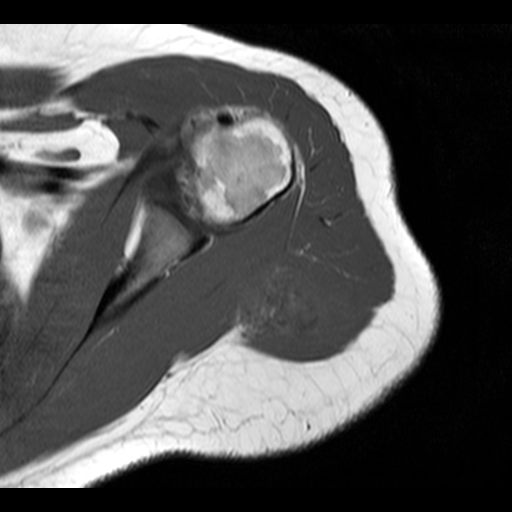
MRI of an extremity soft-tissue mass, one axial slice; position 11 of 20 along the scan axis; 4 mm slice thickness; 512 × 512 image matrix, field of view 150 × 150 mm. Female patient. From the clinical record (not read from this slice): histological type: malignant fibrous histiocytoma; grade: low; site of the primary tumour: left arm.
Annotated regions visible in this slice (manually delineated by an expert):
- gross tumour volume (mass): box from (x=229, y=251) to (x=326, y=342) px